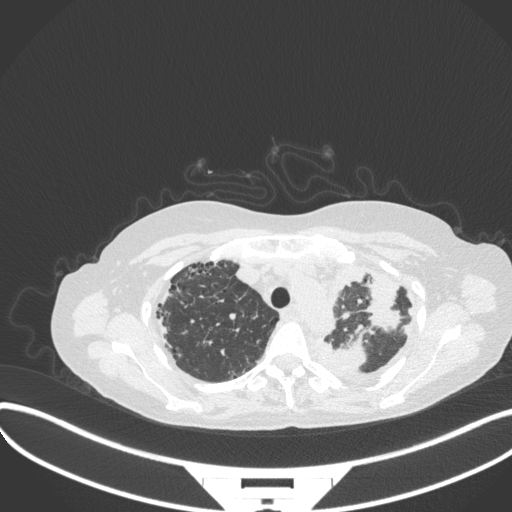
Chest CT, one axial slice. Position 271 of 373 along the scan axis. Reconstruction kernel B31f. 120 kVp. Lung window (W 1500 / L -600 HU). 1 mm slice thickness. 512 × 512 image matrix. Patient: female, 56 years. From the clinical record (not read from this slice): clinical TNM (as recorded): T1 N0 M0.
Outlined on this slice (rectangle marked by the reading radiologist):
- lung tumour (recorded histology: adenocarcinoma): bounding box (x1, y1, x2, y2) in pixels: (335, 334, 369, 373)
- lung tumour (recorded histology: adenocarcinoma): (363, 277, 408, 331)